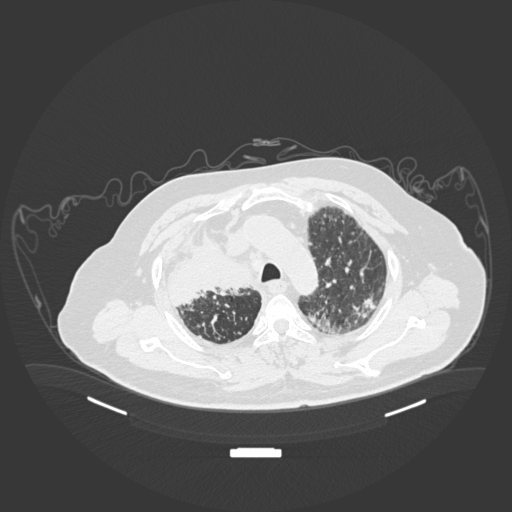
Chest CT, one axial slice; position 144 of 201 along the scan axis; 120 kVp; lung window (W 1500 / L -600 HU); 1 mm slice thickness; 512 × 512 image matrix, field of view 500 × 500 mm. Patient: male, 69 years. From the clinical record (not read from this slice): clinical TNM (as recorded): T4 N3 M1.
Outlined on this slice (bounding box drawn by a radiologist):
- lung tumour (recorded histology: adenocarcinoma): bounding box (x1, y1, x2, y2) in pixels: (162, 221, 257, 309)